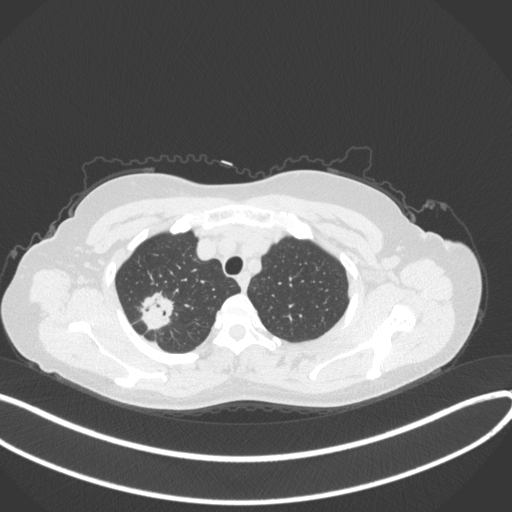
Chest CT, one axial slice; slice 305 of 342 in the series (ordered by position); reconstruction kernel B31f; 120 kVp; lung window (W 1500 / L -600 HU); 1 mm slice thickness; 512 × 512 image matrix. Female patient, age 50 years. Case-level facts recorded for this patient, not image findings: clinical TNM (as recorded): T1c N0 M0.
Annotated regions visible in this slice (rectangle marked by the reading radiologist):
- lung tumour (recorded histology: adenocarcinoma): bounding box (x1, y1, x2, y2) in pixels: (135, 289, 176, 334)